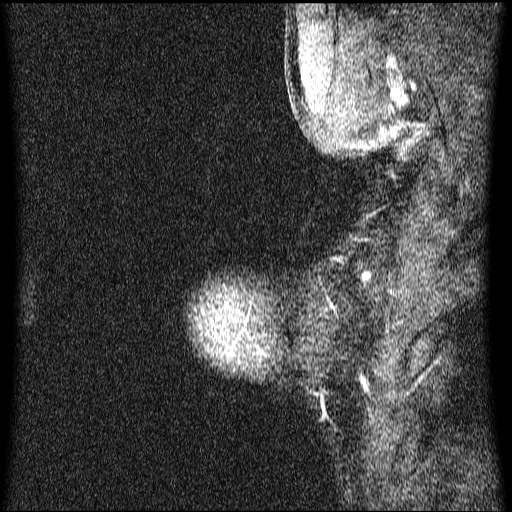
Breast MRI (dynamic contrast-enhanced), one sagittal slice. Slice 59 of 64 in the series (ordered by position). Dynamic contrast-enhanced series, image 2 of 4 at this slice position (ordered by acquisition). 1.5 T. TE 4.2 ms, TR 9.1 ms. 2 mm slice thickness. 512 × 512 image matrix, field of view 180 × 180 mm. Female patient, age 33 years.
Structures marked on this image (semi-automatic segmentation, software-assisted and operator-edited):
- analysis volume of interest (the breast-tissue region the enhancement analysis was run in; not a lesion): bounding box (x1, y1, x2, y2) in pixels: (197, 286, 321, 395)
- tumour enhancement mask (voxels above the 70 % enhancement threshold inside the analysis volume of interest): (230, 348, 234, 356)